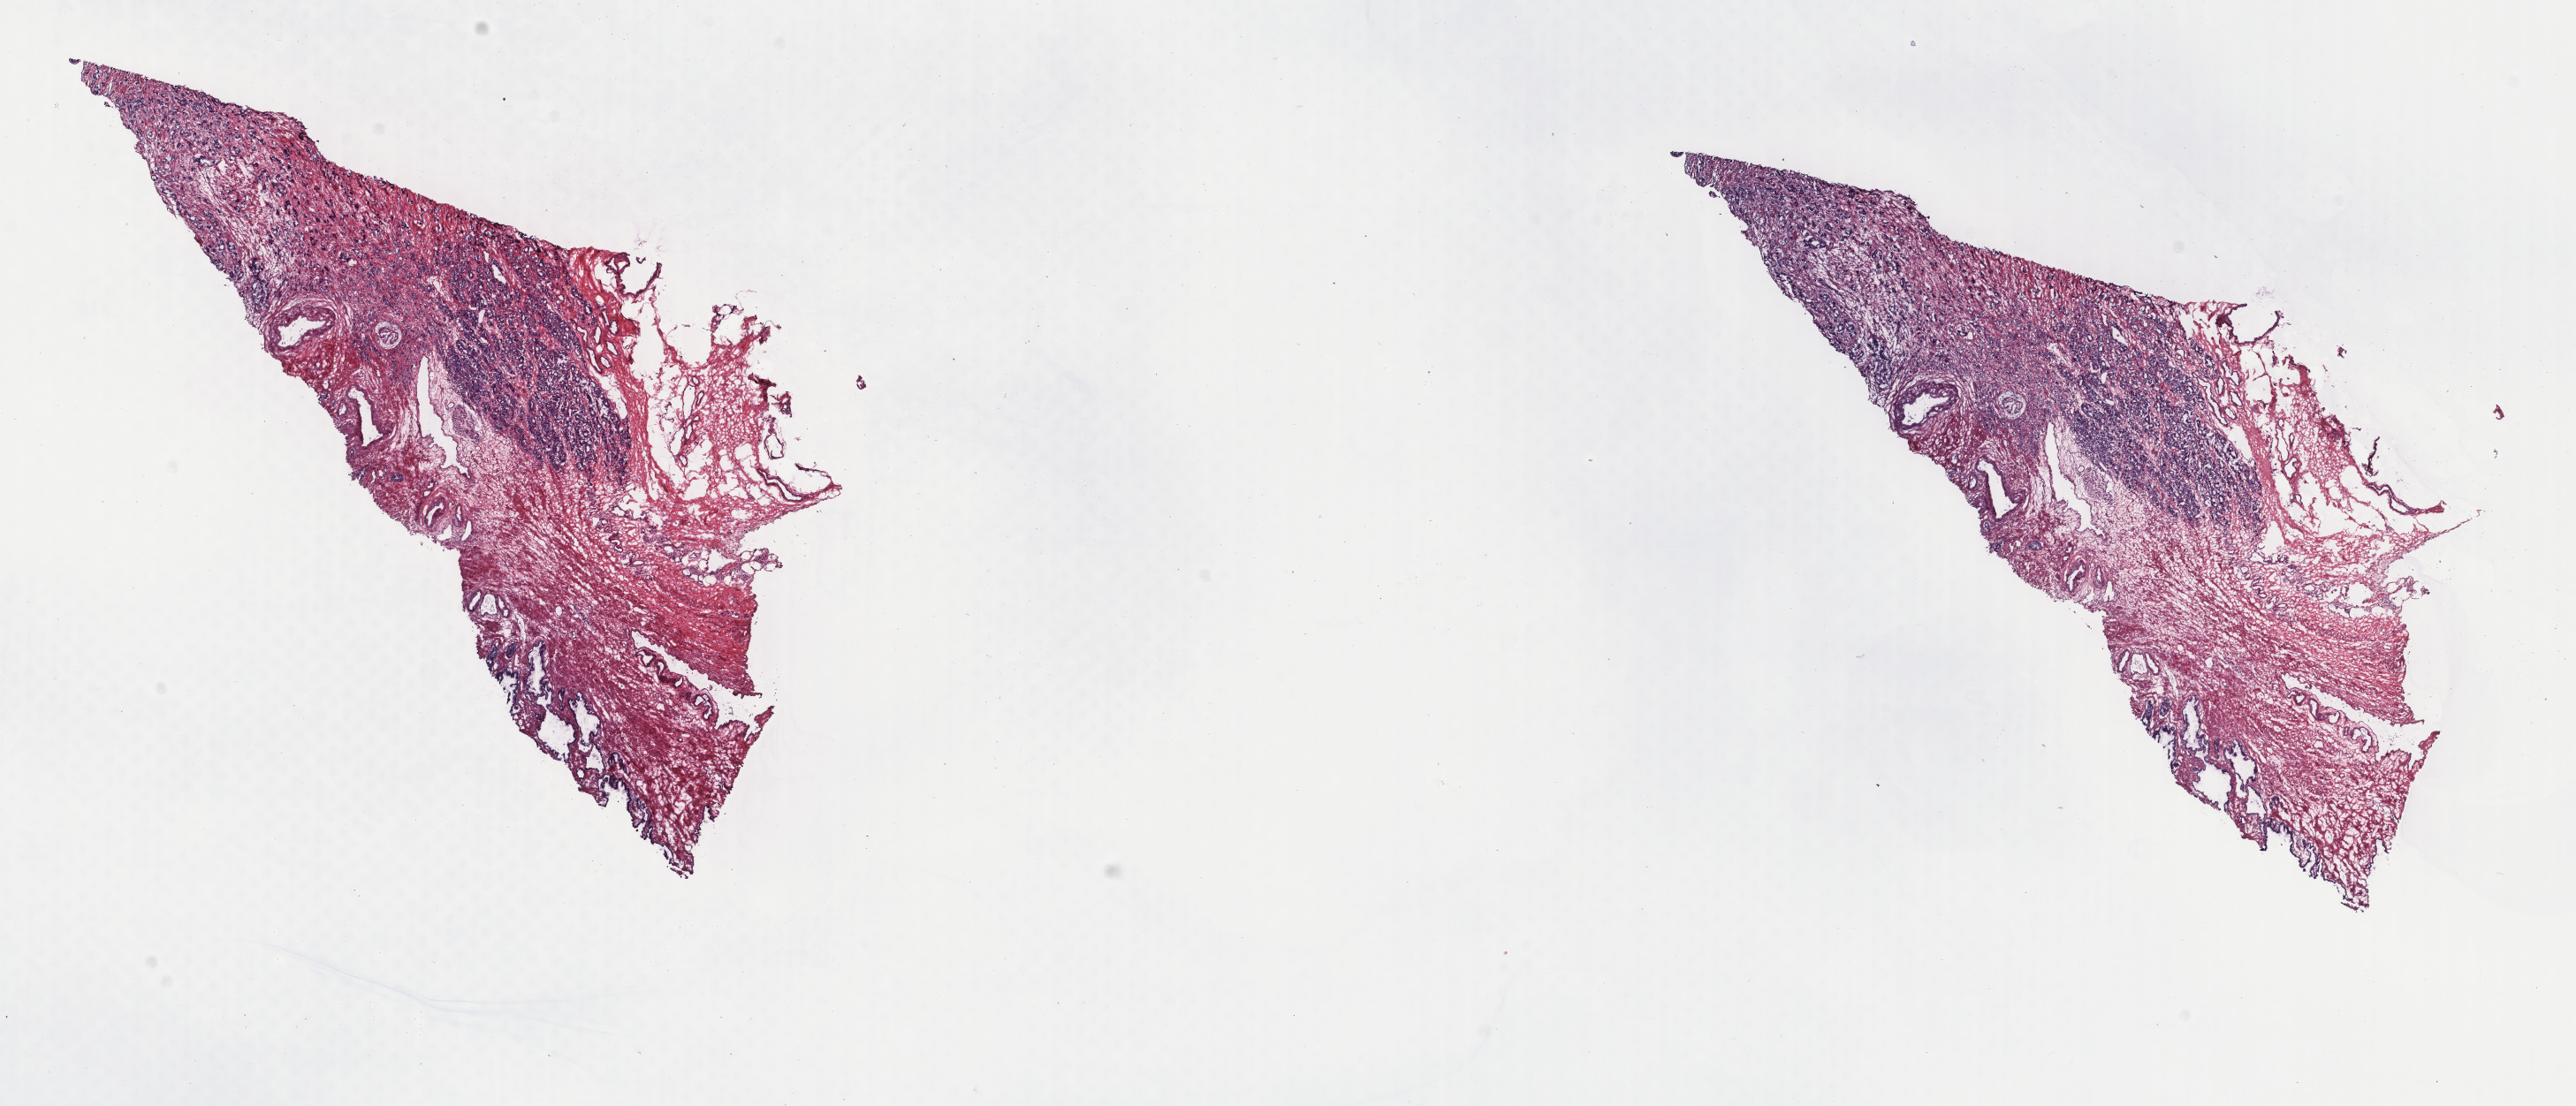
Digitized Hematoxylin and eosin (H&E) stained tissue section (whole slide) — a low-resolution overview of the entire scanned area, about 23.1 x 9.9 mm (slide scanned at 40x); frozen section; primary tumour sample from the prostate. Patient: male, age at initial diagnosis 75 years. Gleason score: 9 (4+5). Composition of this section per pathologist review: tumour cells 40%, tumour nuclei 60%, normal cells 10%, stromal cells 50%, necrosis 0%. Infiltration values recorded for this section: lymphocyte infiltration 0%, monocyte infiltration 0%, neutrophil infiltration 0%.
Laterality: bilateral. Histologic diagnosis: Adenocarcinoma, NOS. Lymph nodes positive (case pathology): 1 of 11 examined.